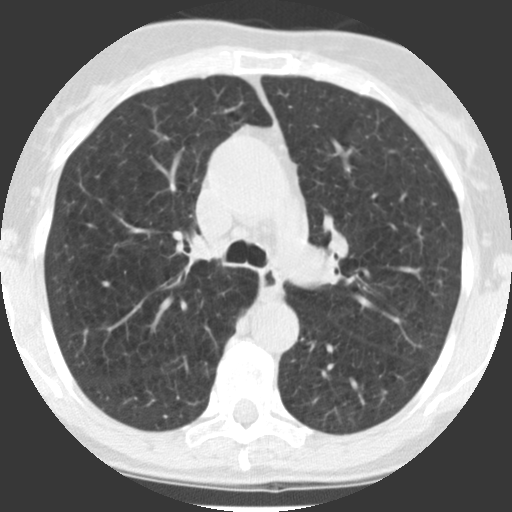
Low-dose screening chest CT, axial slice, baseline screening round, lung window (W 1500 / L -600 HU), 2.5 mm slice thickness, standard (soft-tissue) reconstruction kernel (STANDARD), 120 kVp. Female, age 71 years at enrolment.
• Lesion marked by an expert reader, bounding box (x1, y1, x2, y2) in pixels: (316, 333, 348, 362).
• Screening reader's record for this exam: no non-calcified nodule ≥4 mm recorded.
• Official screen result: negative screen, minor abnormalities not suspicious for lung cancer.
• Later outcome: lung cancer diagnosed 802 days after this screen — squamous cell carcinoma, NOS, left lower lobe, poorly differentiated (G3), stage IB (AJCC 6th edition), 40 mm at pathology.